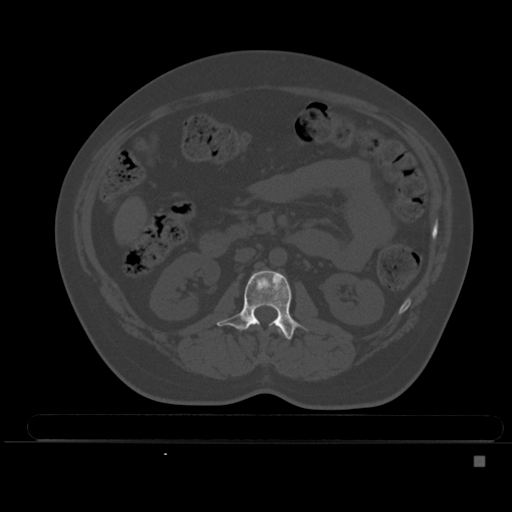
CT including the spine, one axial slice; position 177 of 495 along the scan axis; bone window (W 1800 / L 400 HU); 1.5 mm slice thickness; 512 × 512 image matrix. Patient: female, 33 years. Case-level facts recorded for this patient, not image findings: primary cancer: breast; vertebrae with lytic lesions (as recorded): T1.
Annotated regions visible in this slice (semi-automatic segmentation, software-assisted and operator-edited):
- L1 vertebra: bounding box (x1, y1, x2, y2) in pixels: (277, 326, 285, 337)
- L2 vertebra: (217, 270, 300, 340)